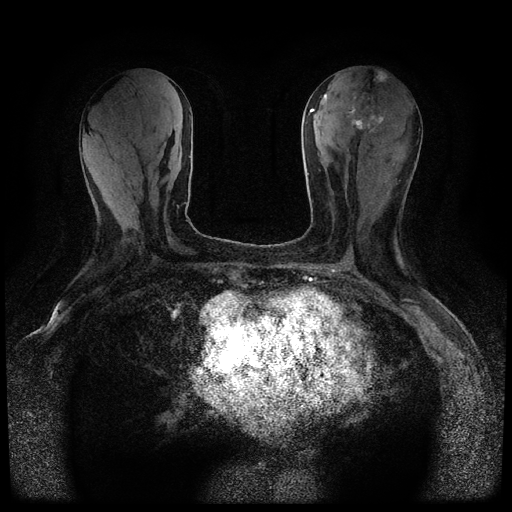
Breast MRI (dynamic contrast-enhanced, multi-phase), one axial slice. Slice 30 of 116 in the series (ordered by position). Dynamic contrast-enhanced series, time point 2 of 5 at this slice position (early post-contrast). 1.5 T. TE 2.7 ms, TR 5.4 ms. 512 × 512 image matrix, field of view 320 × 320 mm. Female patient, age 80 years.
Structures marked on this image (semi-automatically segmented with operator editing):
- breast lesion (labelled 'tumour' in the annotation; benign lesions carry a separate 'benign' label): bounding box <348,70,386,132> (left, top, right, bottom; pixels)